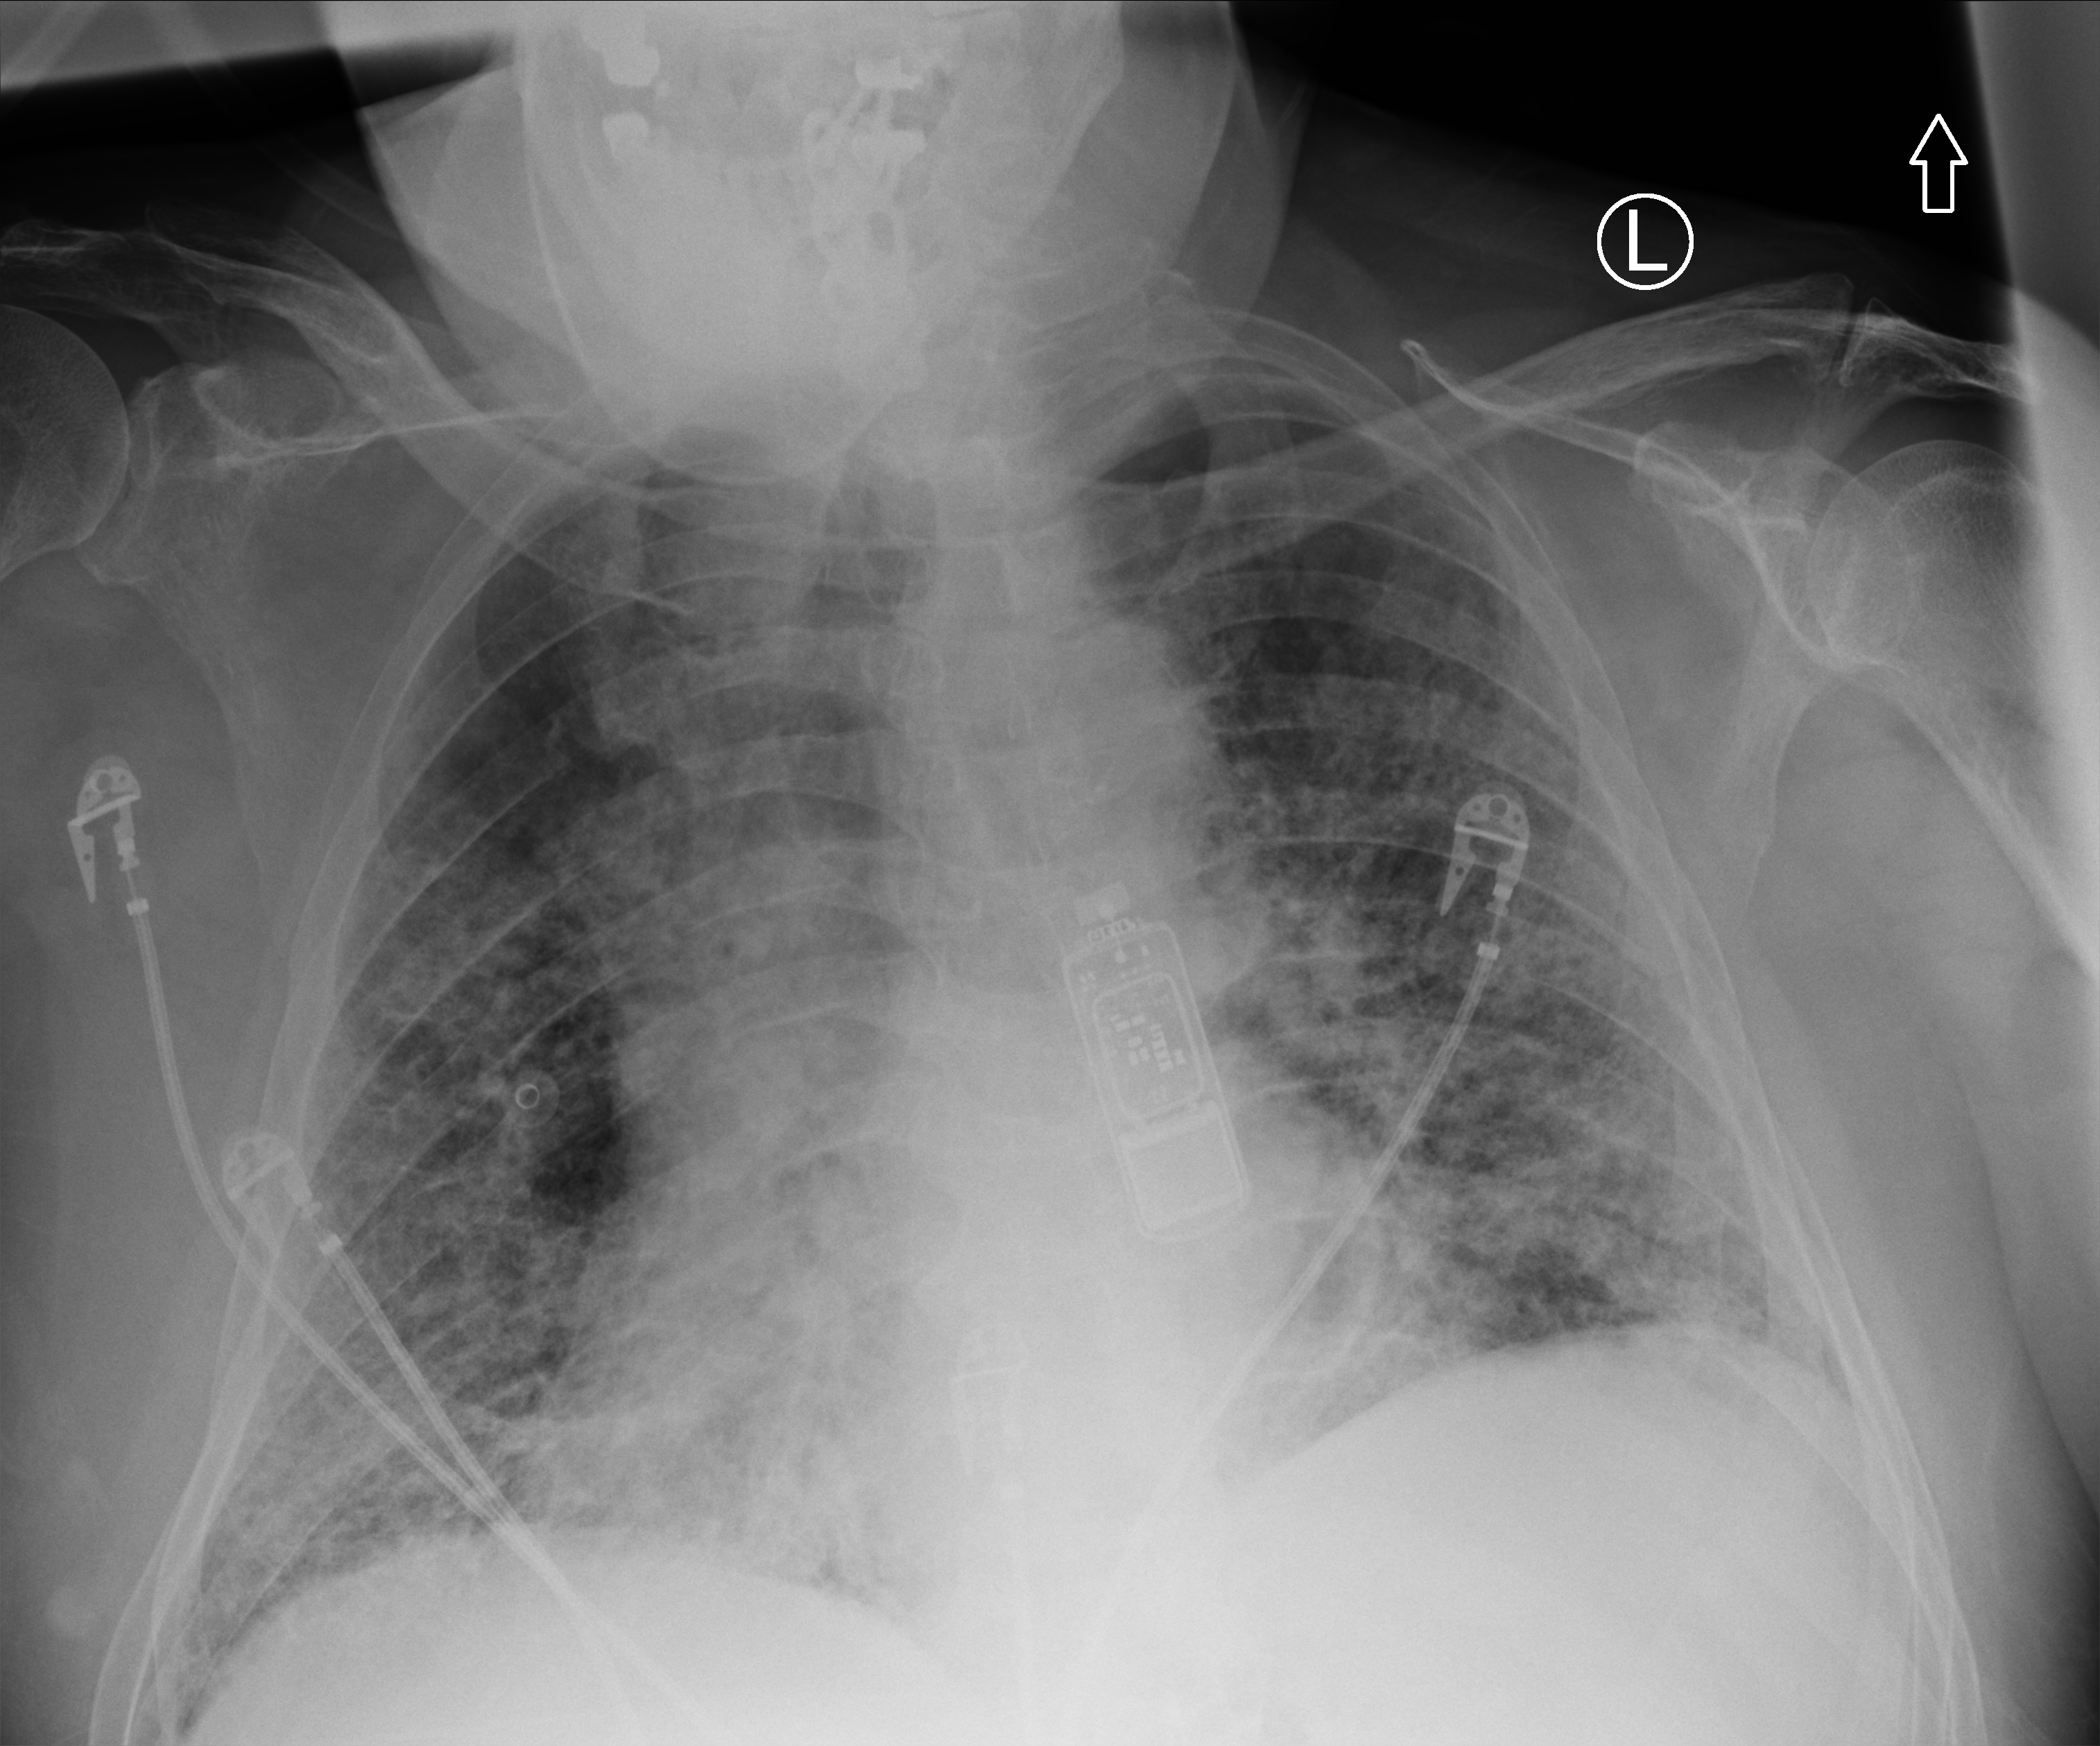
Portable chest radiograph, anteroposterior (AP) projection. Patient hospitalised with COVID-19; male, aged 60–74 years.
Admission-level facts for this patient (not findings on this image; timing relative to this image not recorded): length of hospital stay: 7 days.